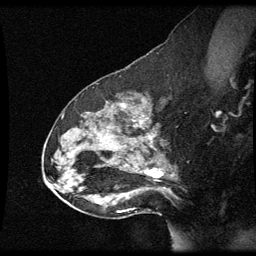
Breast MRI (dynamic contrast-enhanced), one sagittal slice. Slice 36 of 60 in the series (ordered by position). Dynamic contrast-enhanced series, image 2 of 3 at this slice position (ordered by acquisition). 1.5 T. TE 4.2 ms, TR 8.9 ms. 256 × 256 image matrix, field of view 200 × 200 mm. Female patient, age 49 years. Case-level facts recorded for this patient, not image findings: setting: breast cancer imaged before/during neoadjuvant chemotherapy; receptor status: HR-positive, HER2-negative.
Outlined on this slice (semi-automatically segmented with operator editing):
- analysis volume of interest (the breast-tissue region the enhancement analysis was run in; not a lesion): bounding box (x1, y1, x2, y2) in pixels: (46, 92, 177, 205)
- tumour enhancement mask (voxels above the 70 % enhancement threshold inside the analysis volume of interest): (145, 170, 154, 173)